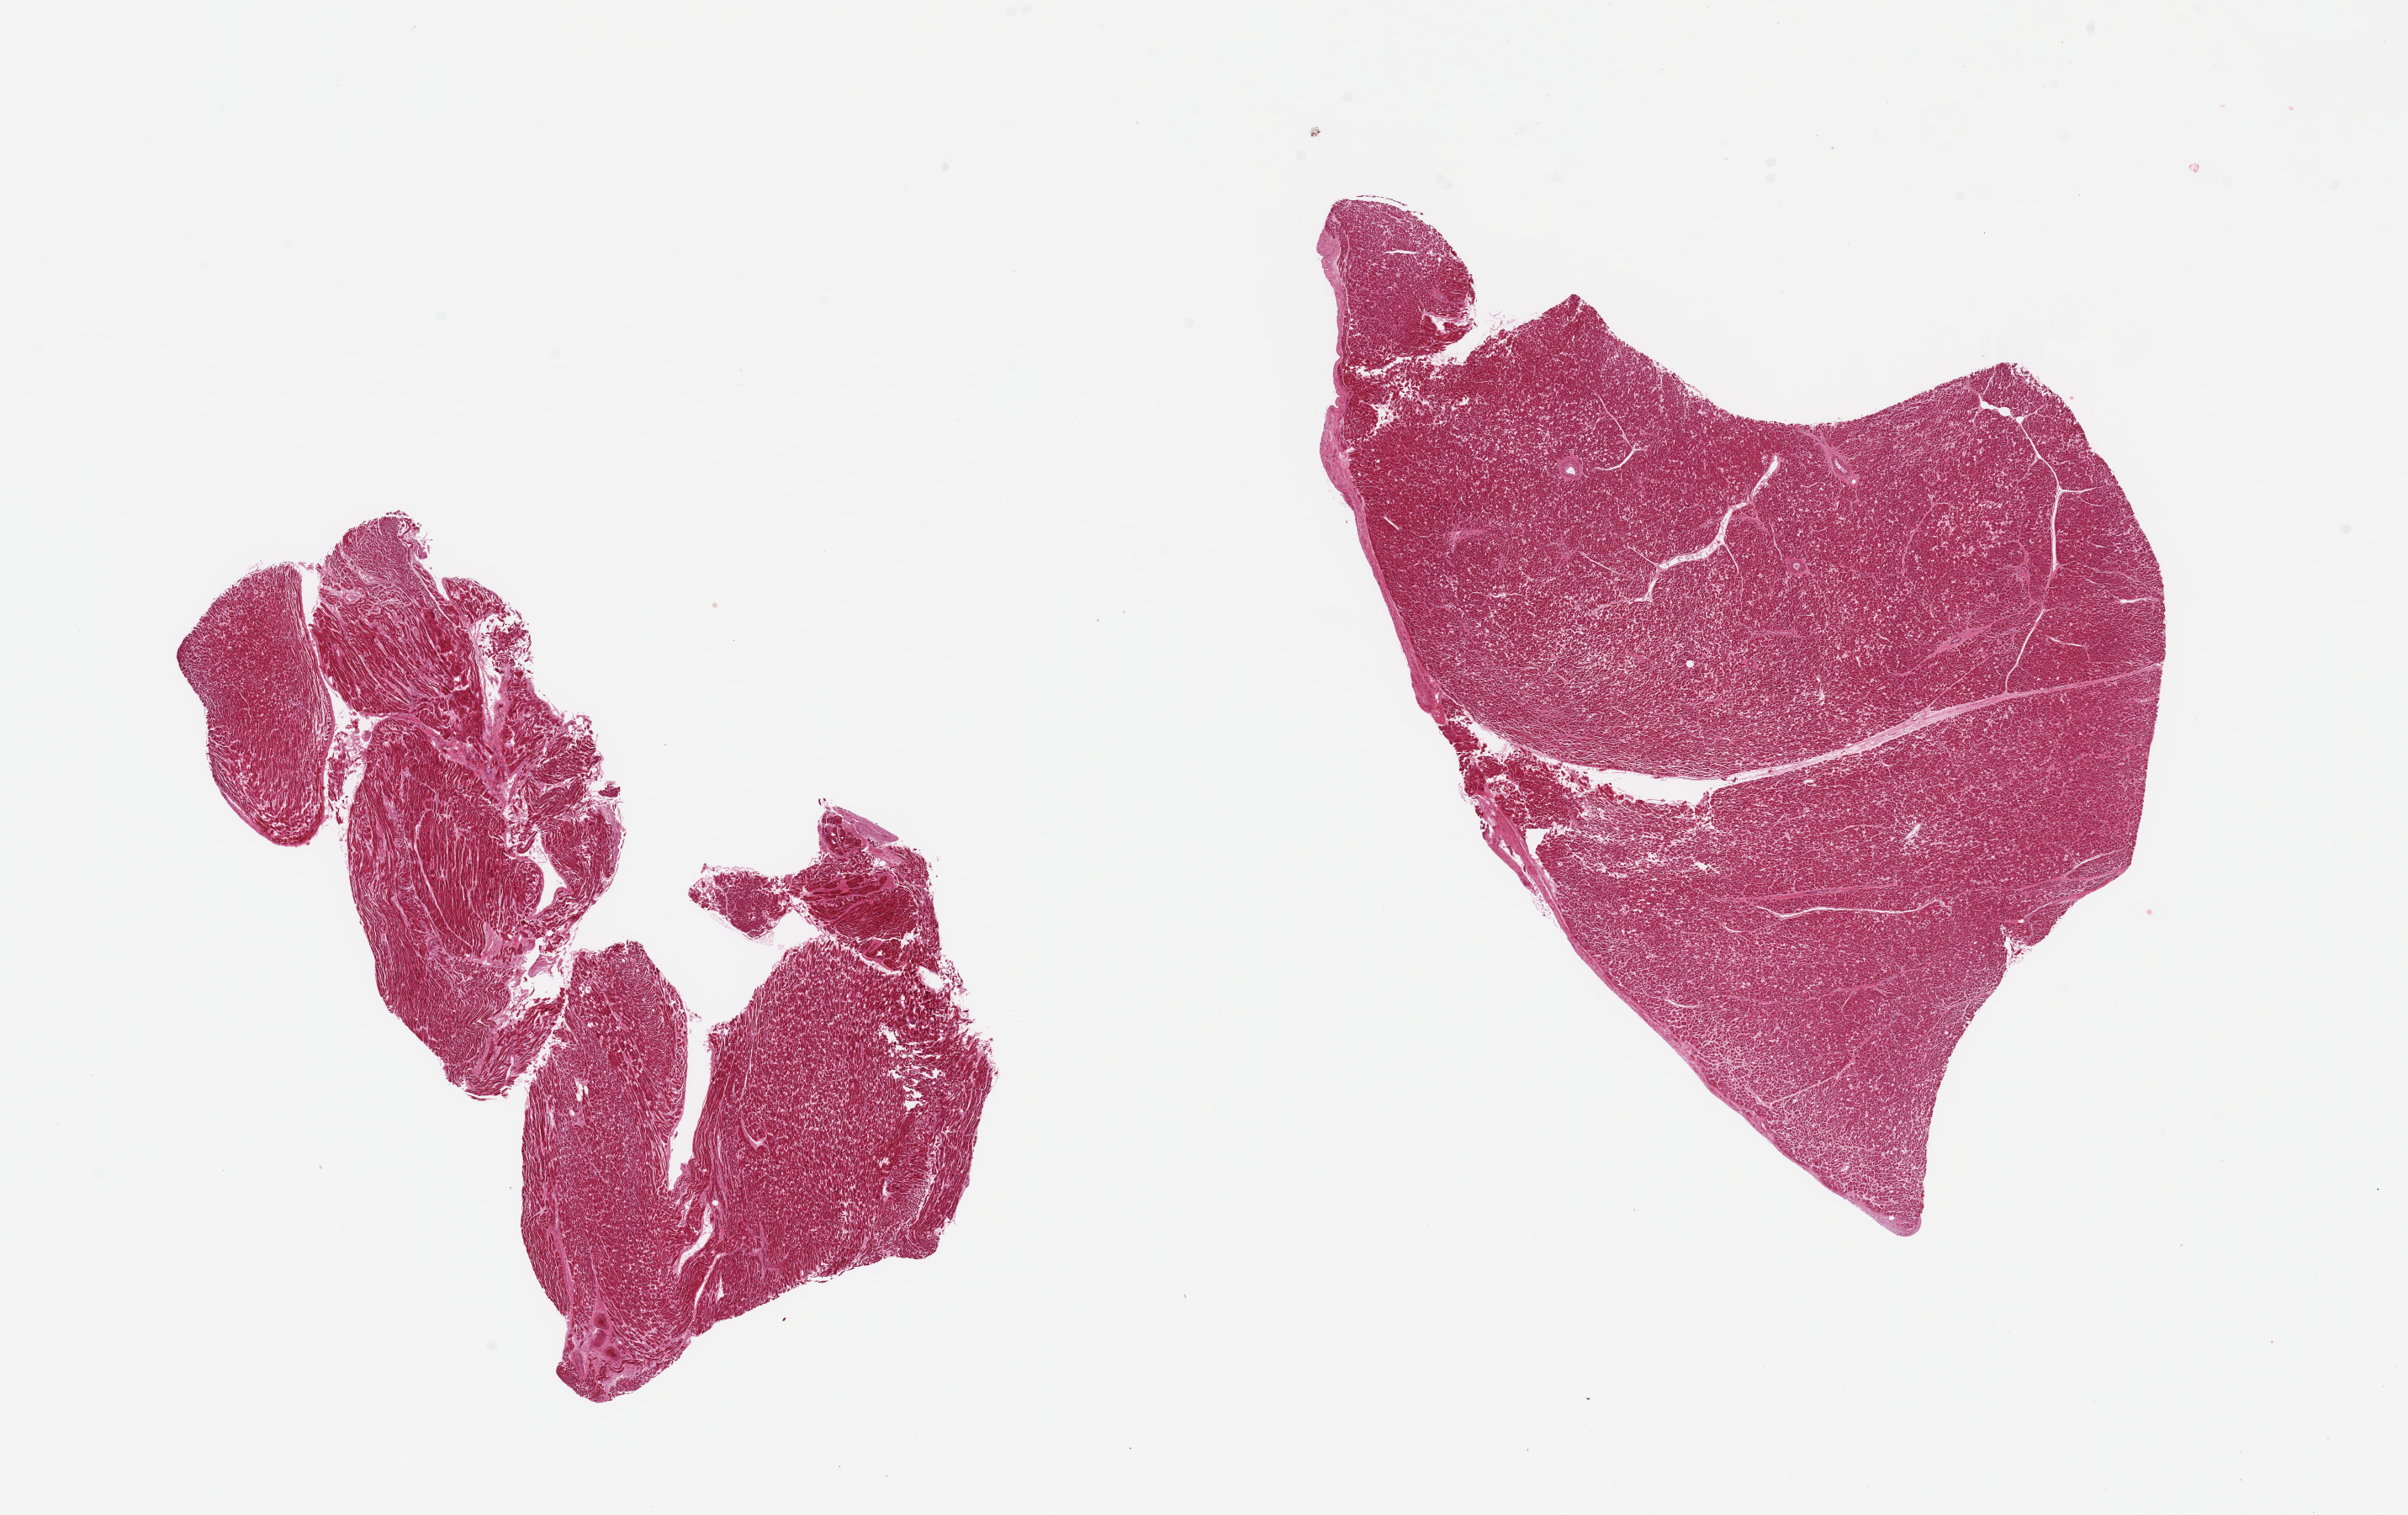
Hematoxylin and eosin (H&E) whole-slide image — shown as a low-resolution overview of the whole scanned area (about 22.6 x 14.2 mm); PAXgene-fixed, paraffin-embedded tissue; section of heart (target tissue); donor tissue sample. Female donor.
* reviewer comment on this tissue sample: 2 pieces